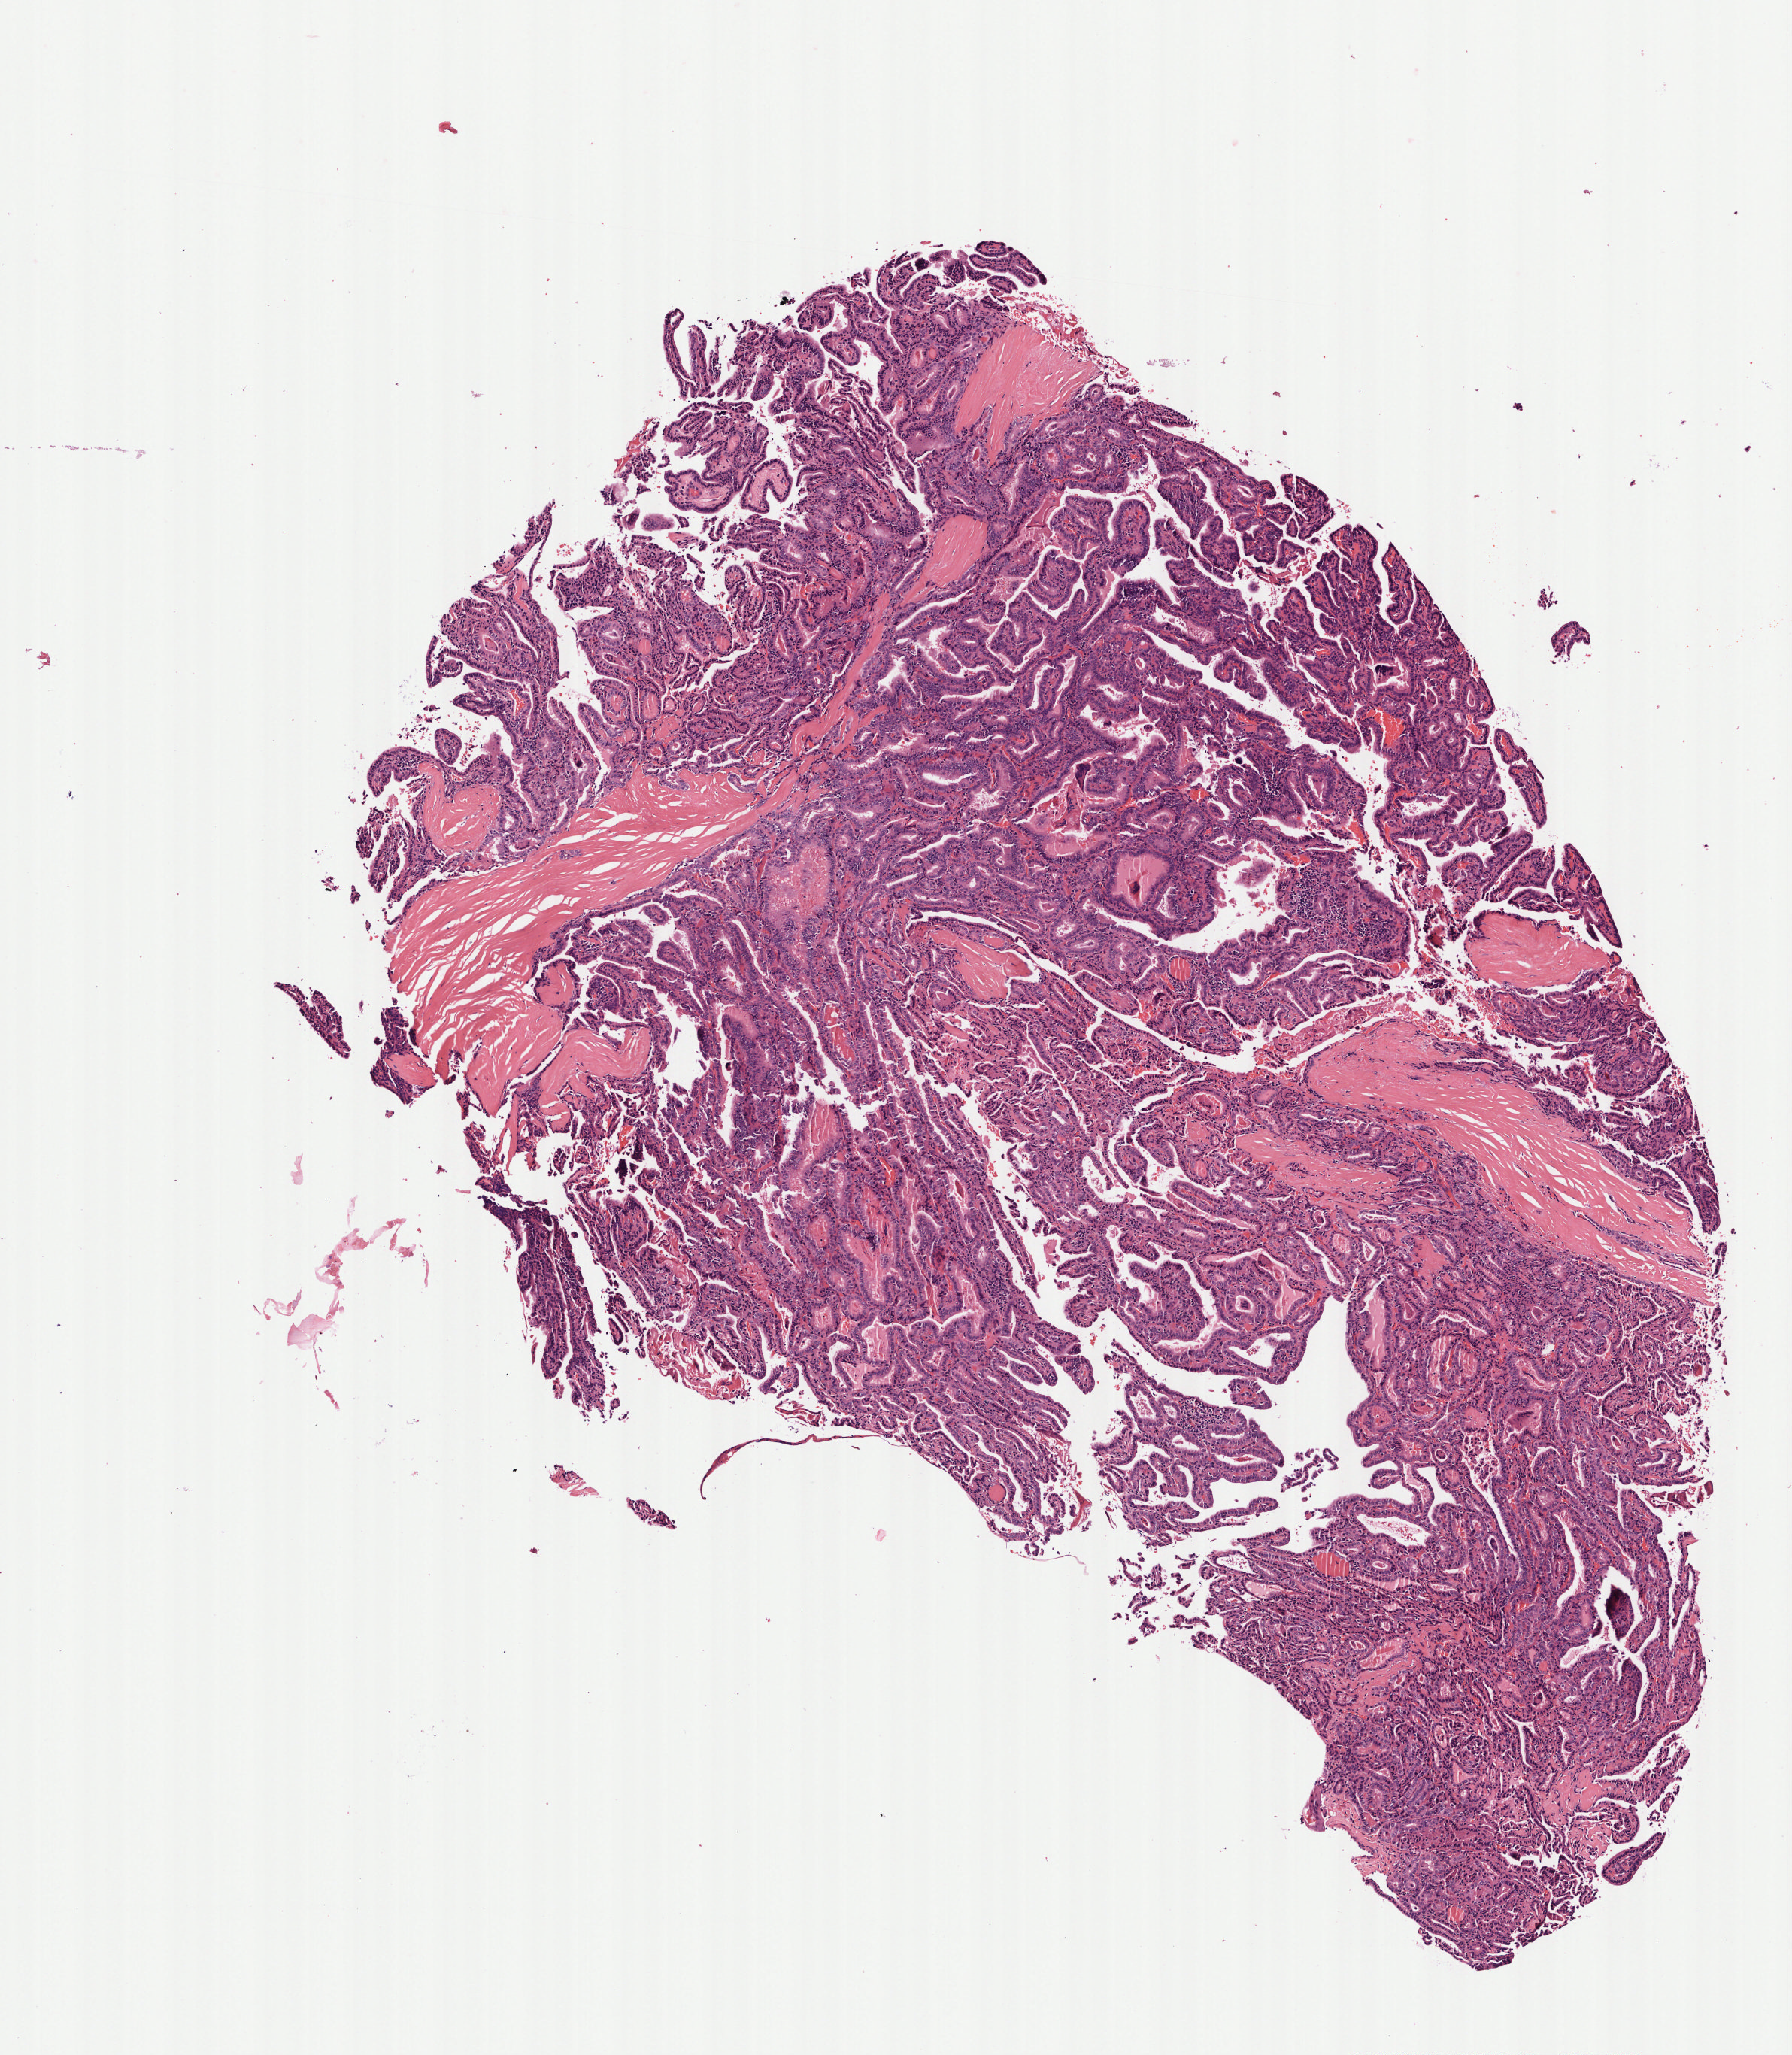
Whole-slide histology image, H&E-stained — shown as a low-resolution overview of the whole scanned area (about 4.8 x 5.5 mm); formalin-fixed paraffin-embedded (FFPE) diagnostic section; thyroid, primary tumour sample. Female patient; age at initial diagnosis 40 years.
* AJCC pathologic stage: I
* lymph nodes positive (case pathology): 1 of 4 examined
* histologic diagnosis: Papillary adenocarcinoma, NOS (thyroid gland)